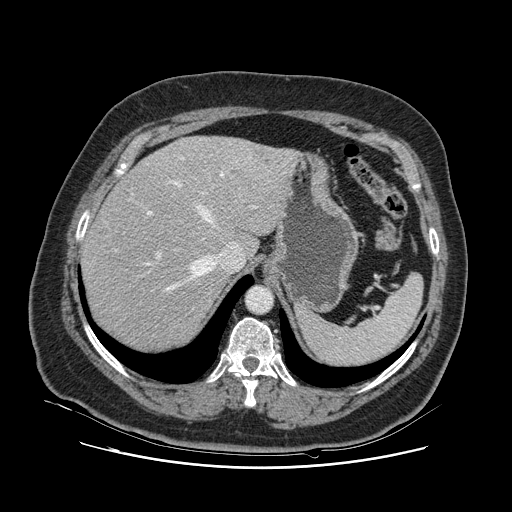
Contrast-enhanced abdominal CT, one axial slice. Position 91 of 132 along the scan axis. Intravenous contrast given. Soft-tissue window (W 400 / L 40 HU). 512 × 512 image matrix, field of view 391 × 391 mm. Female patient, age 73 years. From the clinical record (not read from this slice): diagnosis: colorectal cancer liver metastases, imaged before liver resection; multiple liver metastases: no; largest metastasis: 7 cm; disease in both lobes: no.
Annotated regions visible in this slice (expert manual segmentation):
- hepatic veins: bounding box [x1, y1, x2, y2] px = [123, 158, 251, 291]
- liver: [83, 137, 292, 351]
- planned liver remnant (the part of the liver to remain after resection): [83, 160, 249, 351]
- portal vein (with intrahepatic branches): [115, 157, 184, 260]